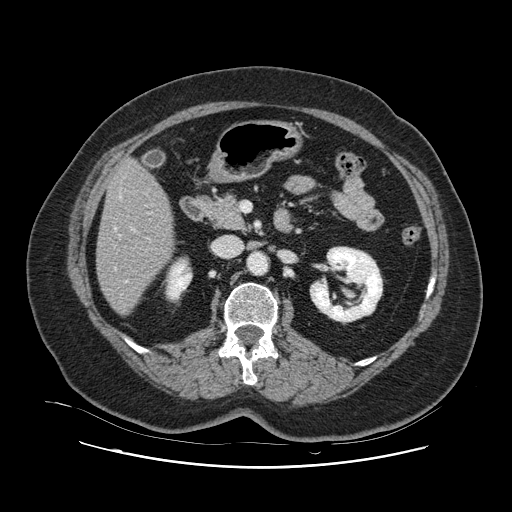
Contrast-enhanced abdominal CT, one axial slice; position 40 of 132 along the scan axis; intravenous contrast given; soft-tissue window (W 400 / L 40 HU); 2.5 mm slice thickness; 512 × 512 image matrix. Female patient, age 73 years. Case-level facts recorded for this patient, not image findings: diagnosis: colorectal cancer liver metastases, imaged before liver resection; multiple liver metastases: no; largest metastasis: 7 cm; disease in both lobes: no.
Annotated regions visible in this slice (manually delineated by an expert):
- hepatic veins: box from (x=114, y=195) to (x=122, y=270) px
- liver: (x=97, y=160)–(x=174, y=314)
- planned liver remnant (the part of the liver to remain after resection): (x=97, y=160)–(x=174, y=314)
- portal vein (with intrahepatic branches): (x=125, y=228)–(x=135, y=283)